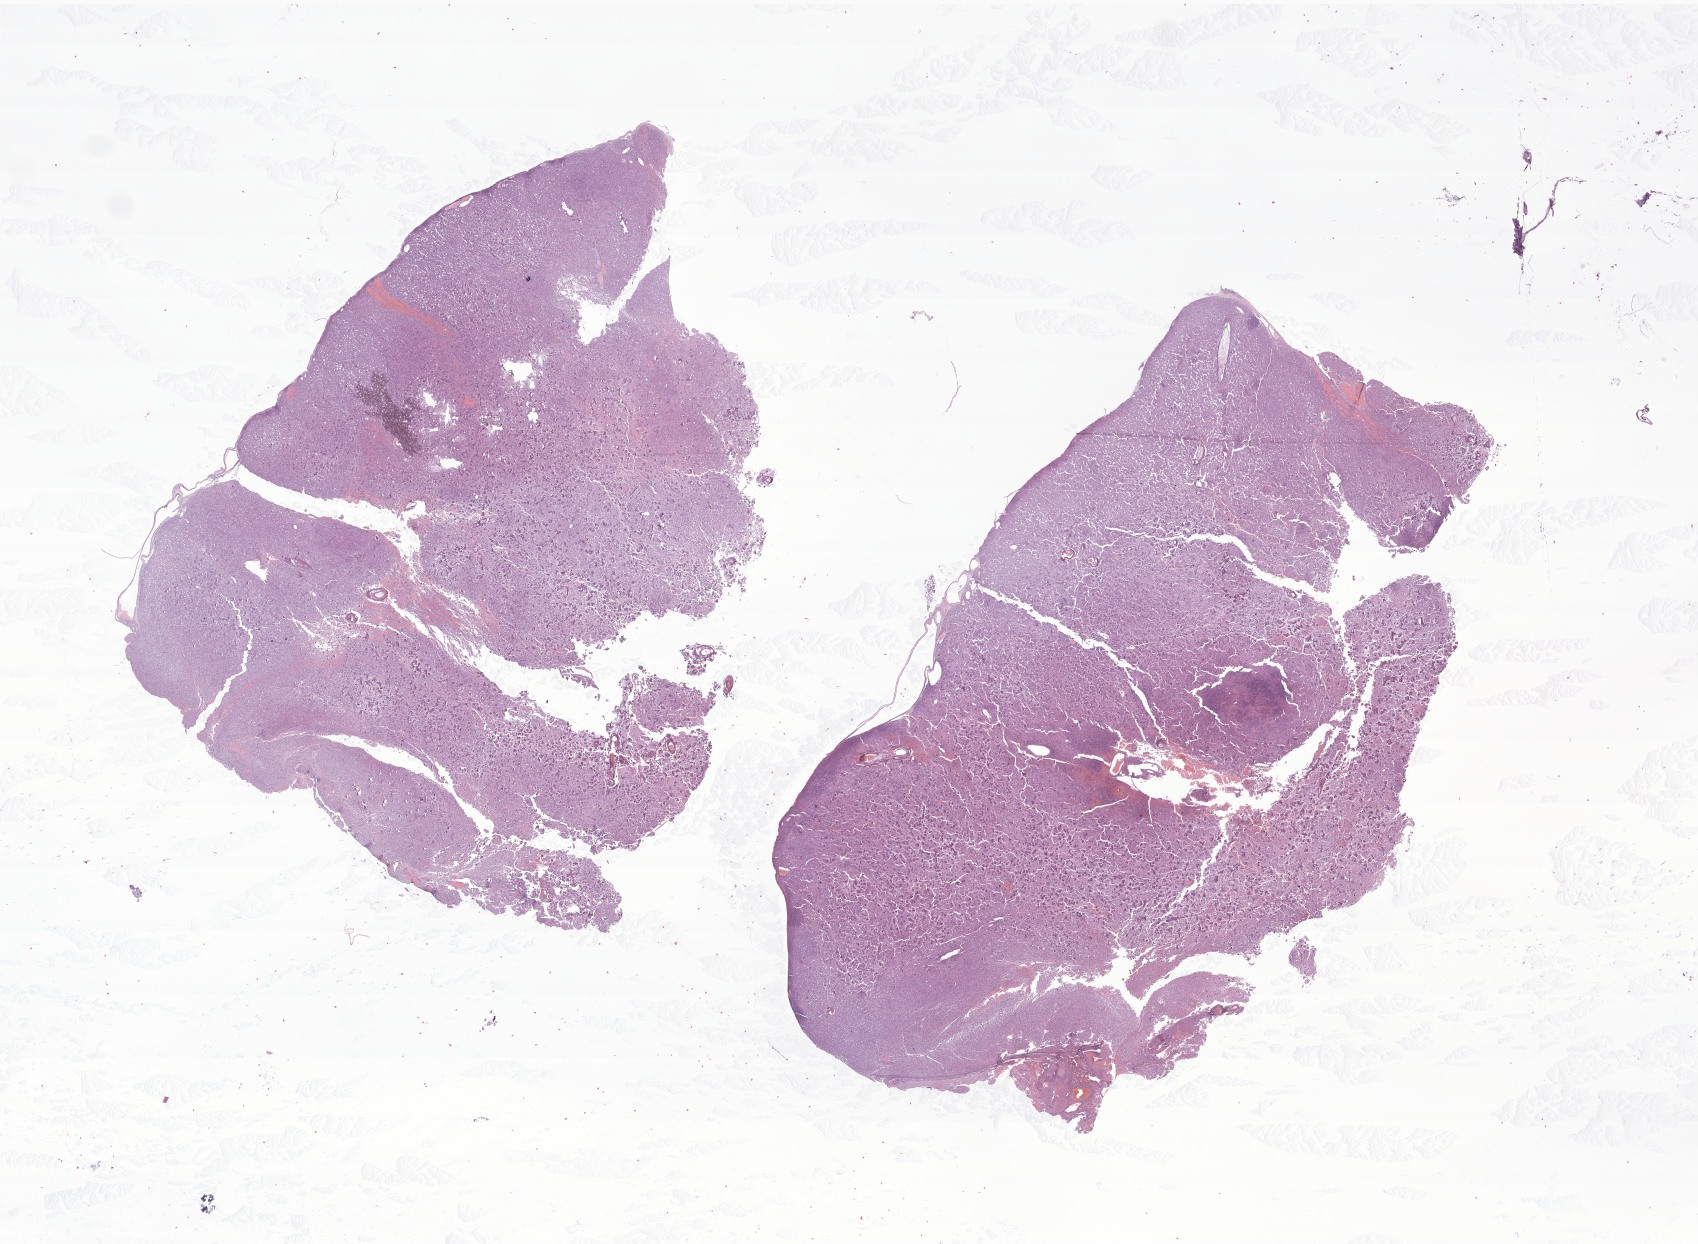
Whole-slide image, H&E stain of tumor tissue from the frontal lobe — a low-resolution overview of the entire scanned area, about 28.6 x 21.0 mm, FFPE section. Patient male; age 35 months (2 years 11 months).
Diagnosis (ICD-O-3 morphology term): Ependymoma, anaplastic.